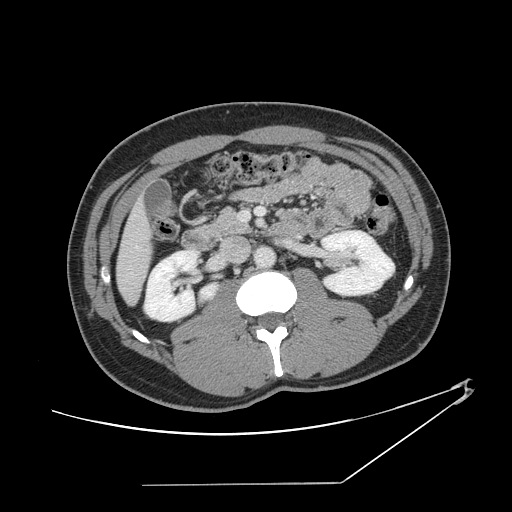
Contrast-enhanced abdominal CT, one axial slice. Position 53 of 152 along the scan axis. 120 kVp. Intravenous contrast given. Soft-tissue window (W 400 / L 40 HU). 512 × 512 image matrix. Male patient, age 45 years. From the clinical record (not read from this slice): diagnosis: colorectal cancer liver metastases, imaged before liver resection; multiple liver metastases: no; largest metastasis: 1 cm; chemotherapy before resection: yes.
Structures marked on this image (outlined manually by an expert reader):
- hepatic veins: bounding box [x1, y1, x2, y2] px = [135, 245, 140, 250]
- liver: [118, 205, 150, 303]
- planned liver remnant (the part of the liver to remain after resection): [118, 205, 150, 303]
- portal vein (with intrahepatic branches): [241, 207, 265, 221]